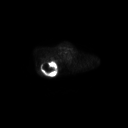
FDG PET of an extremity soft-tissue mass (from a PET/CT study), one axial slice. Slice 215 of 267 in the series (ordered by position). 3.27 mm slice thickness. 128 × 128 image matrix, field of view 700 × 700 mm. Patient: male, 61 years. From the clinical record (not read from this slice): histological type: pleiomorphic spindle cell undifferentiated; grade: high; site of the primary tumour: right parascapusular.
Annotated regions visible in this slice (expert contour drawn on MRI and transferred to this co-registered scan by the dataset authors):
- gross tumour volume including surrounding oedema: bounding box <39,60,60,75> (left, top, right, bottom; pixels)
- gross tumour volume (mass): <41,61,56,75>